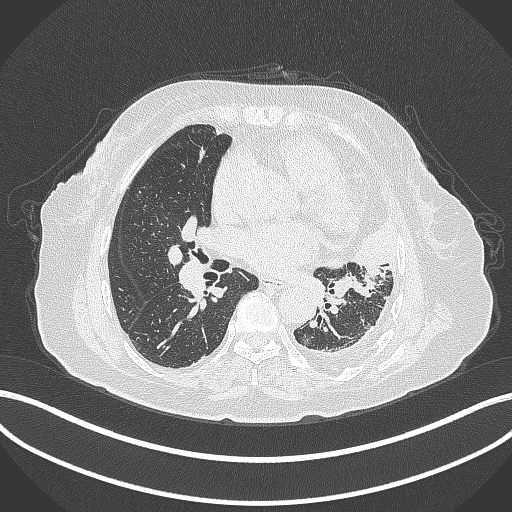
Chest CT, one axial slice; position 179 of 399 along the scan axis; reconstruction kernel B70f; 120 kVp; lung window (W 1500 / L -600 HU); 512 × 512 image matrix. Female patient, age 75 years. Case-level facts recorded for this patient, not image findings: clinical TNM (as recorded): T3 N3 M1.
Annotated regions visible in this slice (rectangle marked by the reading radiologist):
- lung tumour (recorded histology: adenocarcinoma): bounding box [x1, y1, x2, y2] px = [321, 217, 401, 274]